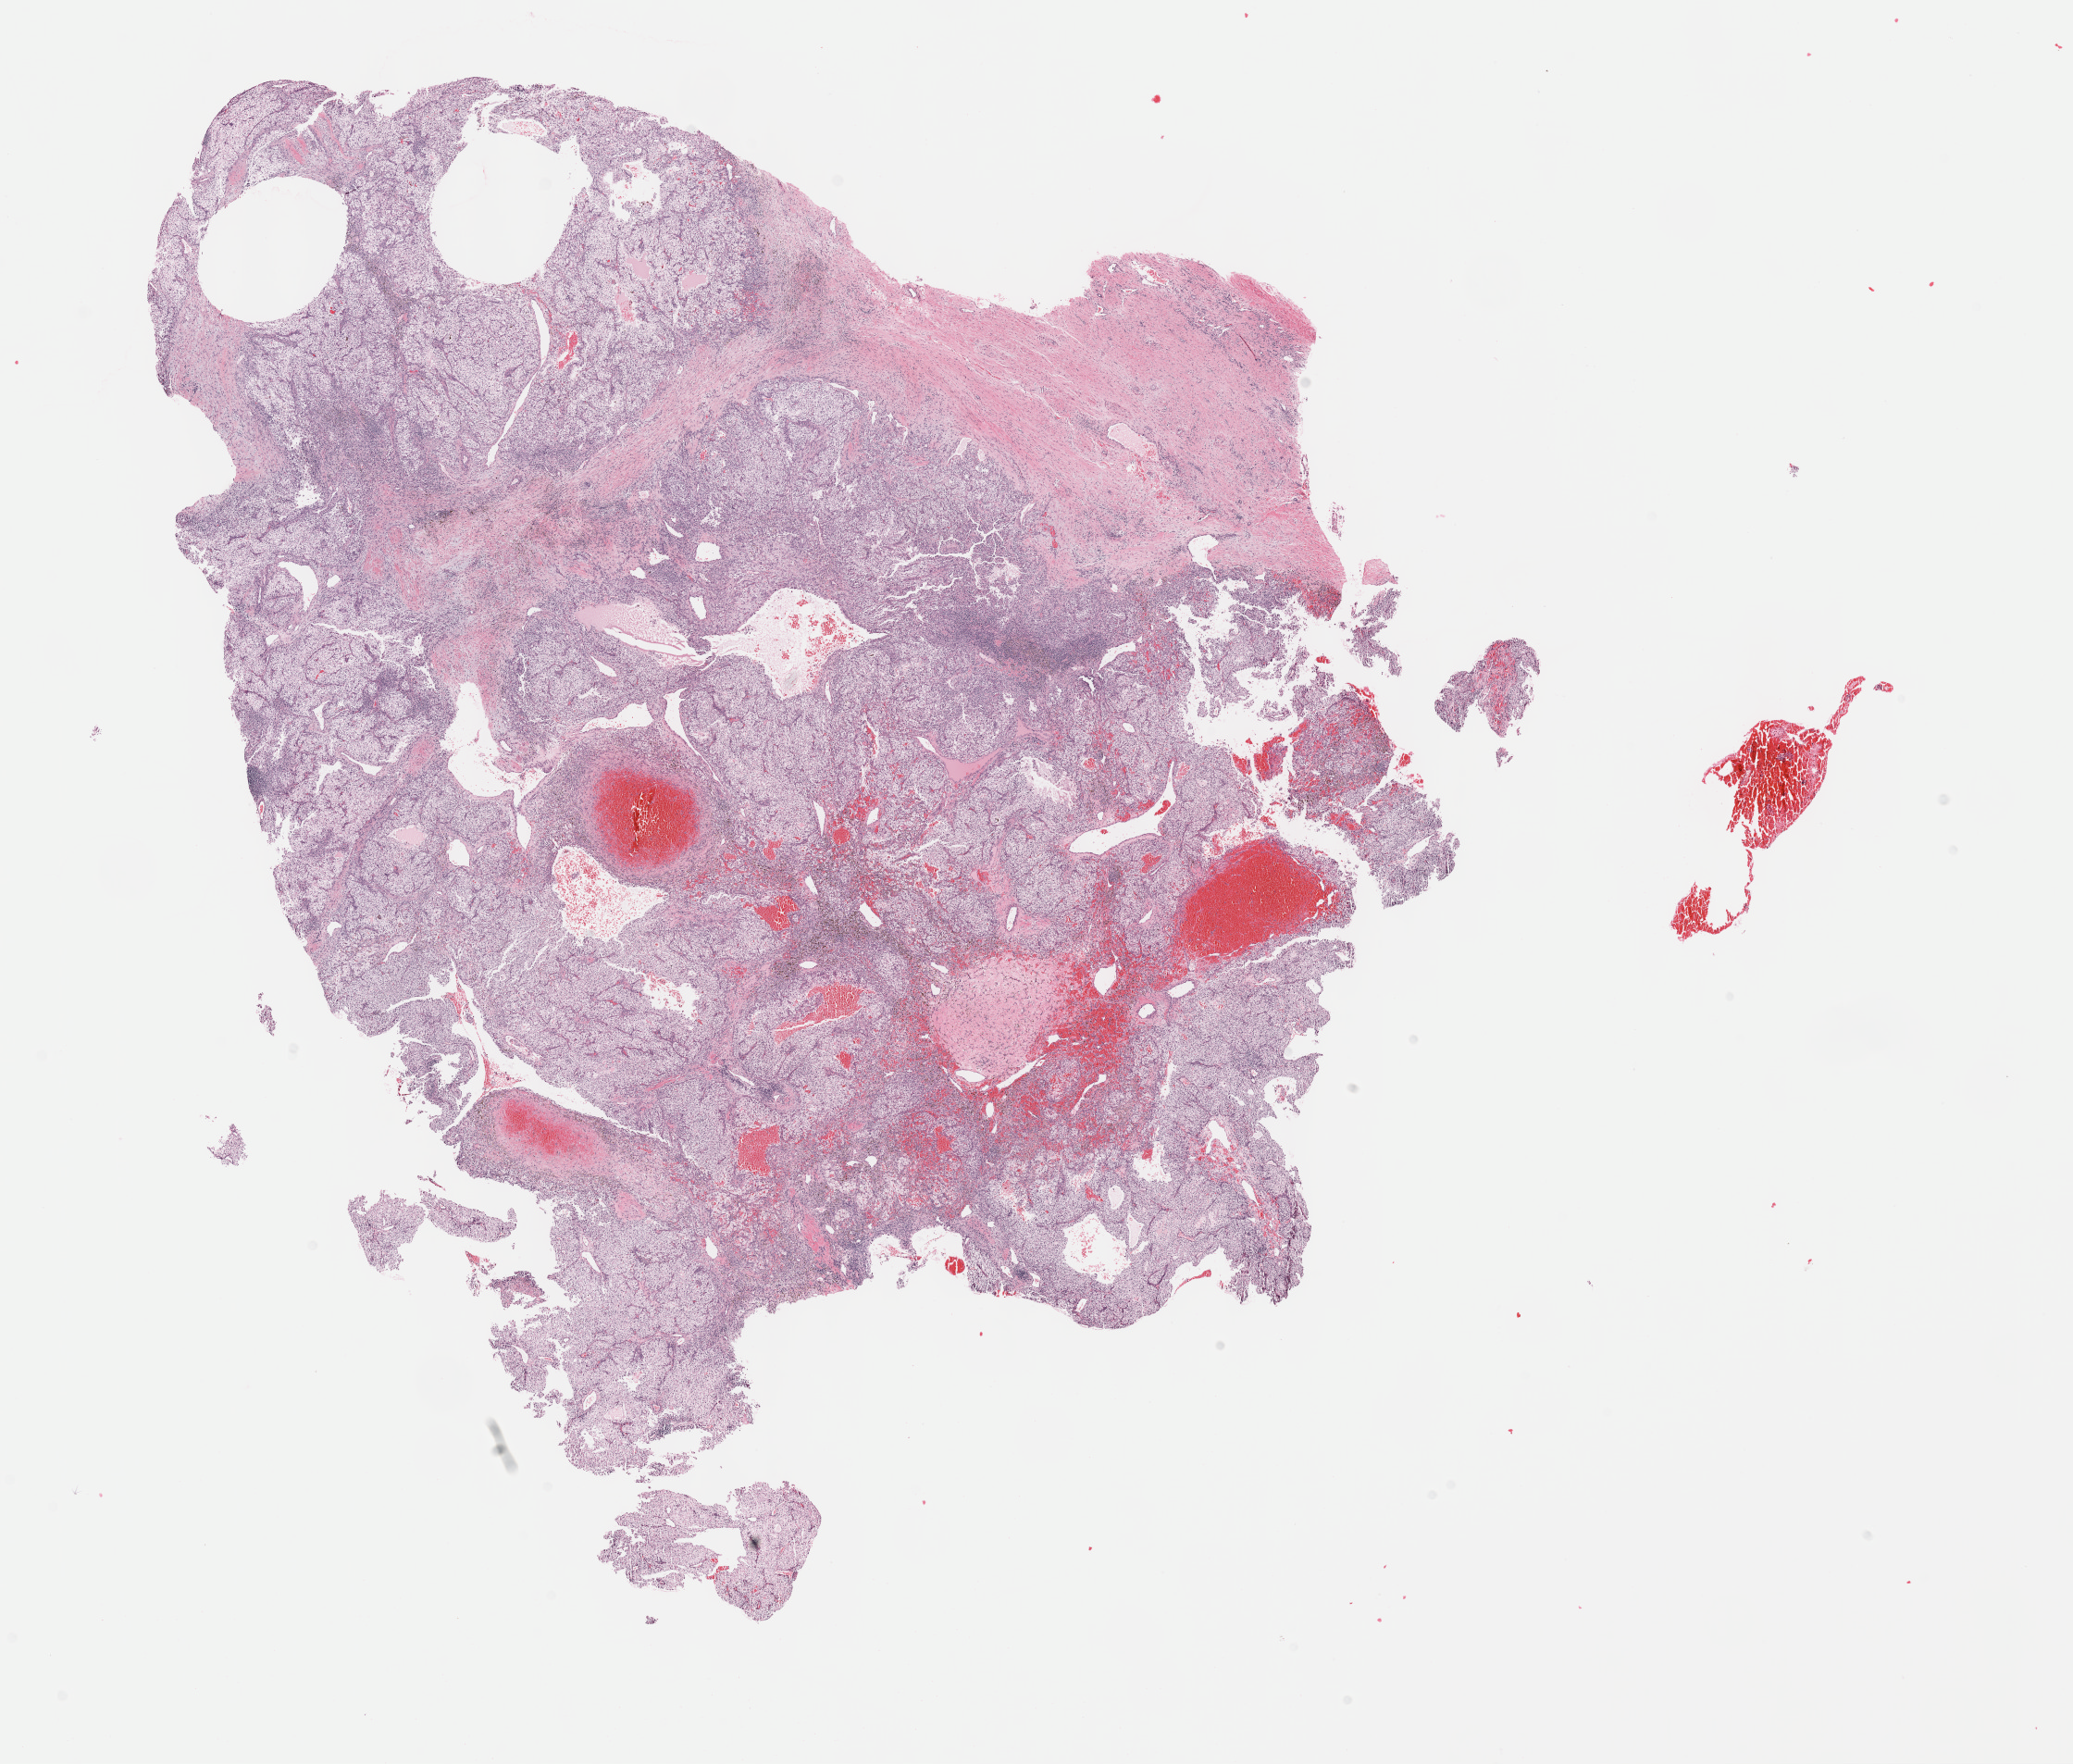
Whole-slide histology image, Hematoxylin and eosin (H&E) stained, low-resolution overview of the scanned area, about 18.1 x 15.4 mm. Formalin-fixed paraffin-embedded (FFPE) diagnostic section. Sample: primary tumour, kidney. Male patient; age at initial diagnosis 68 years. Histologic grade: G2 (moderately differentiated).
AJCC pathologic stage: I. TNM: T1 N0 M0. Laterality: left. Histologic diagnosis: Clear cell adenocarcinoma, NOS. Lymph nodes positive (case pathology): 0 of 6 examined.